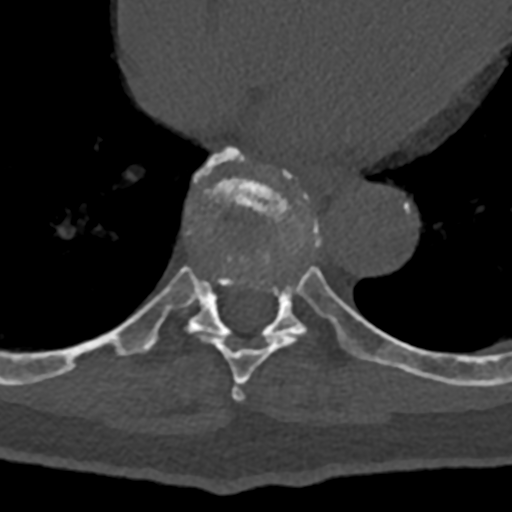
CT including the spine, one axial slice; reconstruction kernel Br40s/3; 120 kVp; bone window (W 1800 / L 400 HU); 0.5 mm slice thickness; 512 × 512 image matrix. Male patient, age 74 years. Case-level facts recorded for this patient, not image findings: primary cancer: renal; vertebrae with lytic lesions (as recorded): T10, L1, L2, L3, L4, L5.
Outlined on this slice (semi-automatically segmented with operator editing):
- T7 vertebra: bounding box <232,383,244,401> (left, top, right, bottom; pixels)
- T8 vertebra: <70,178,343,384>
- T9 vertebra: <80,148,432,379>